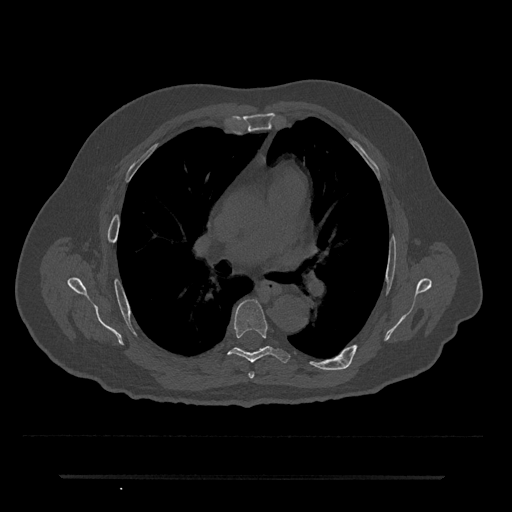
CT including the spine, one axial slice; slice 436 of 797 in the series (ordered by position); reconstruction kernel Br40s/3; 120 kVp; bone window (W 1800 / L 400 HU); 0.5 mm slice thickness; 512 × 512 image matrix, field of view 437 × 437 mm. Male patient, age 69 years. From the clinical record (not read from this slice): primary cancer: prostate.
Annotated regions visible in this slice (semi-automatic segmentation, software-assisted and operator-edited):
- T5 vertebra: bounding box <248,372,255,379> (left, top, right, bottom; pixels)
- T6 vertebra: <229,299,289,363>